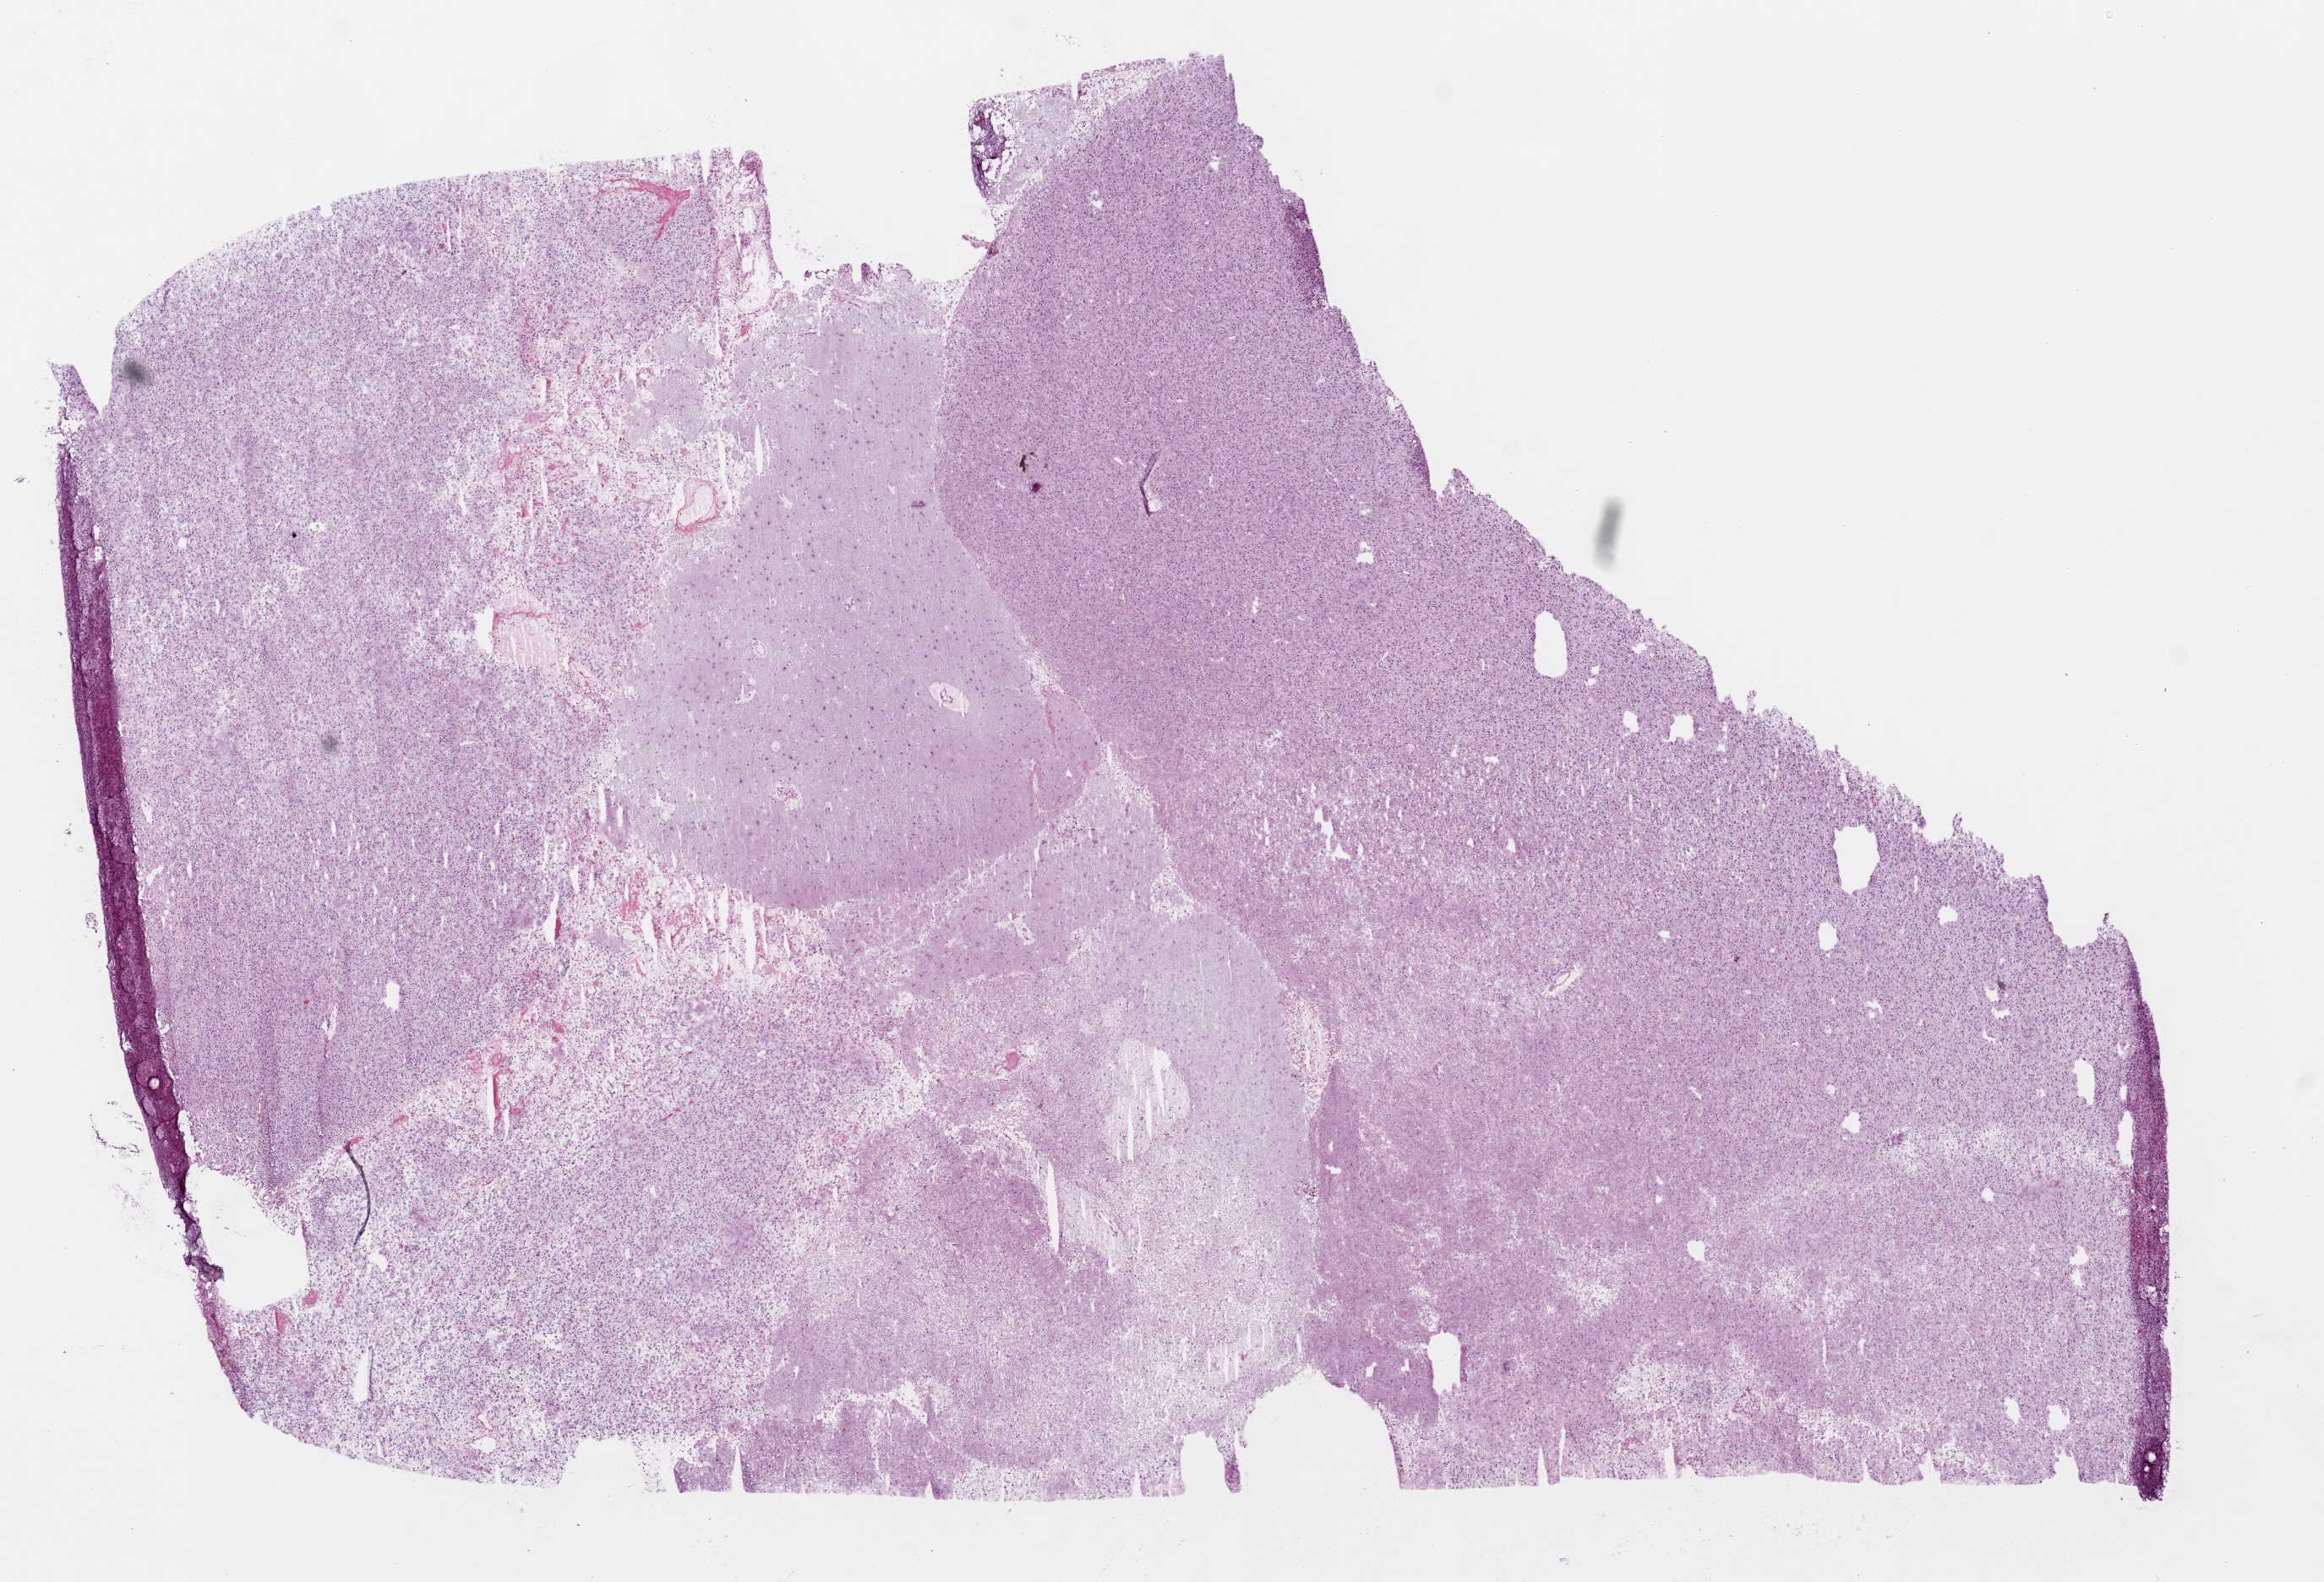
Whole-slide histology image, H&E — whole scanned area (about 11.0 x 7.5 mm, from a 20x scan) shown as a low-resolution overview, frozen section from the top of the tissue portion, brain, primary tumour sample. Male patient; age at initial diagnosis 50 years. Slide review estimates, as recorded: tumour cells 98%, tumour nuclei 80%.
Histologic diagnosis: Glioblastoma.